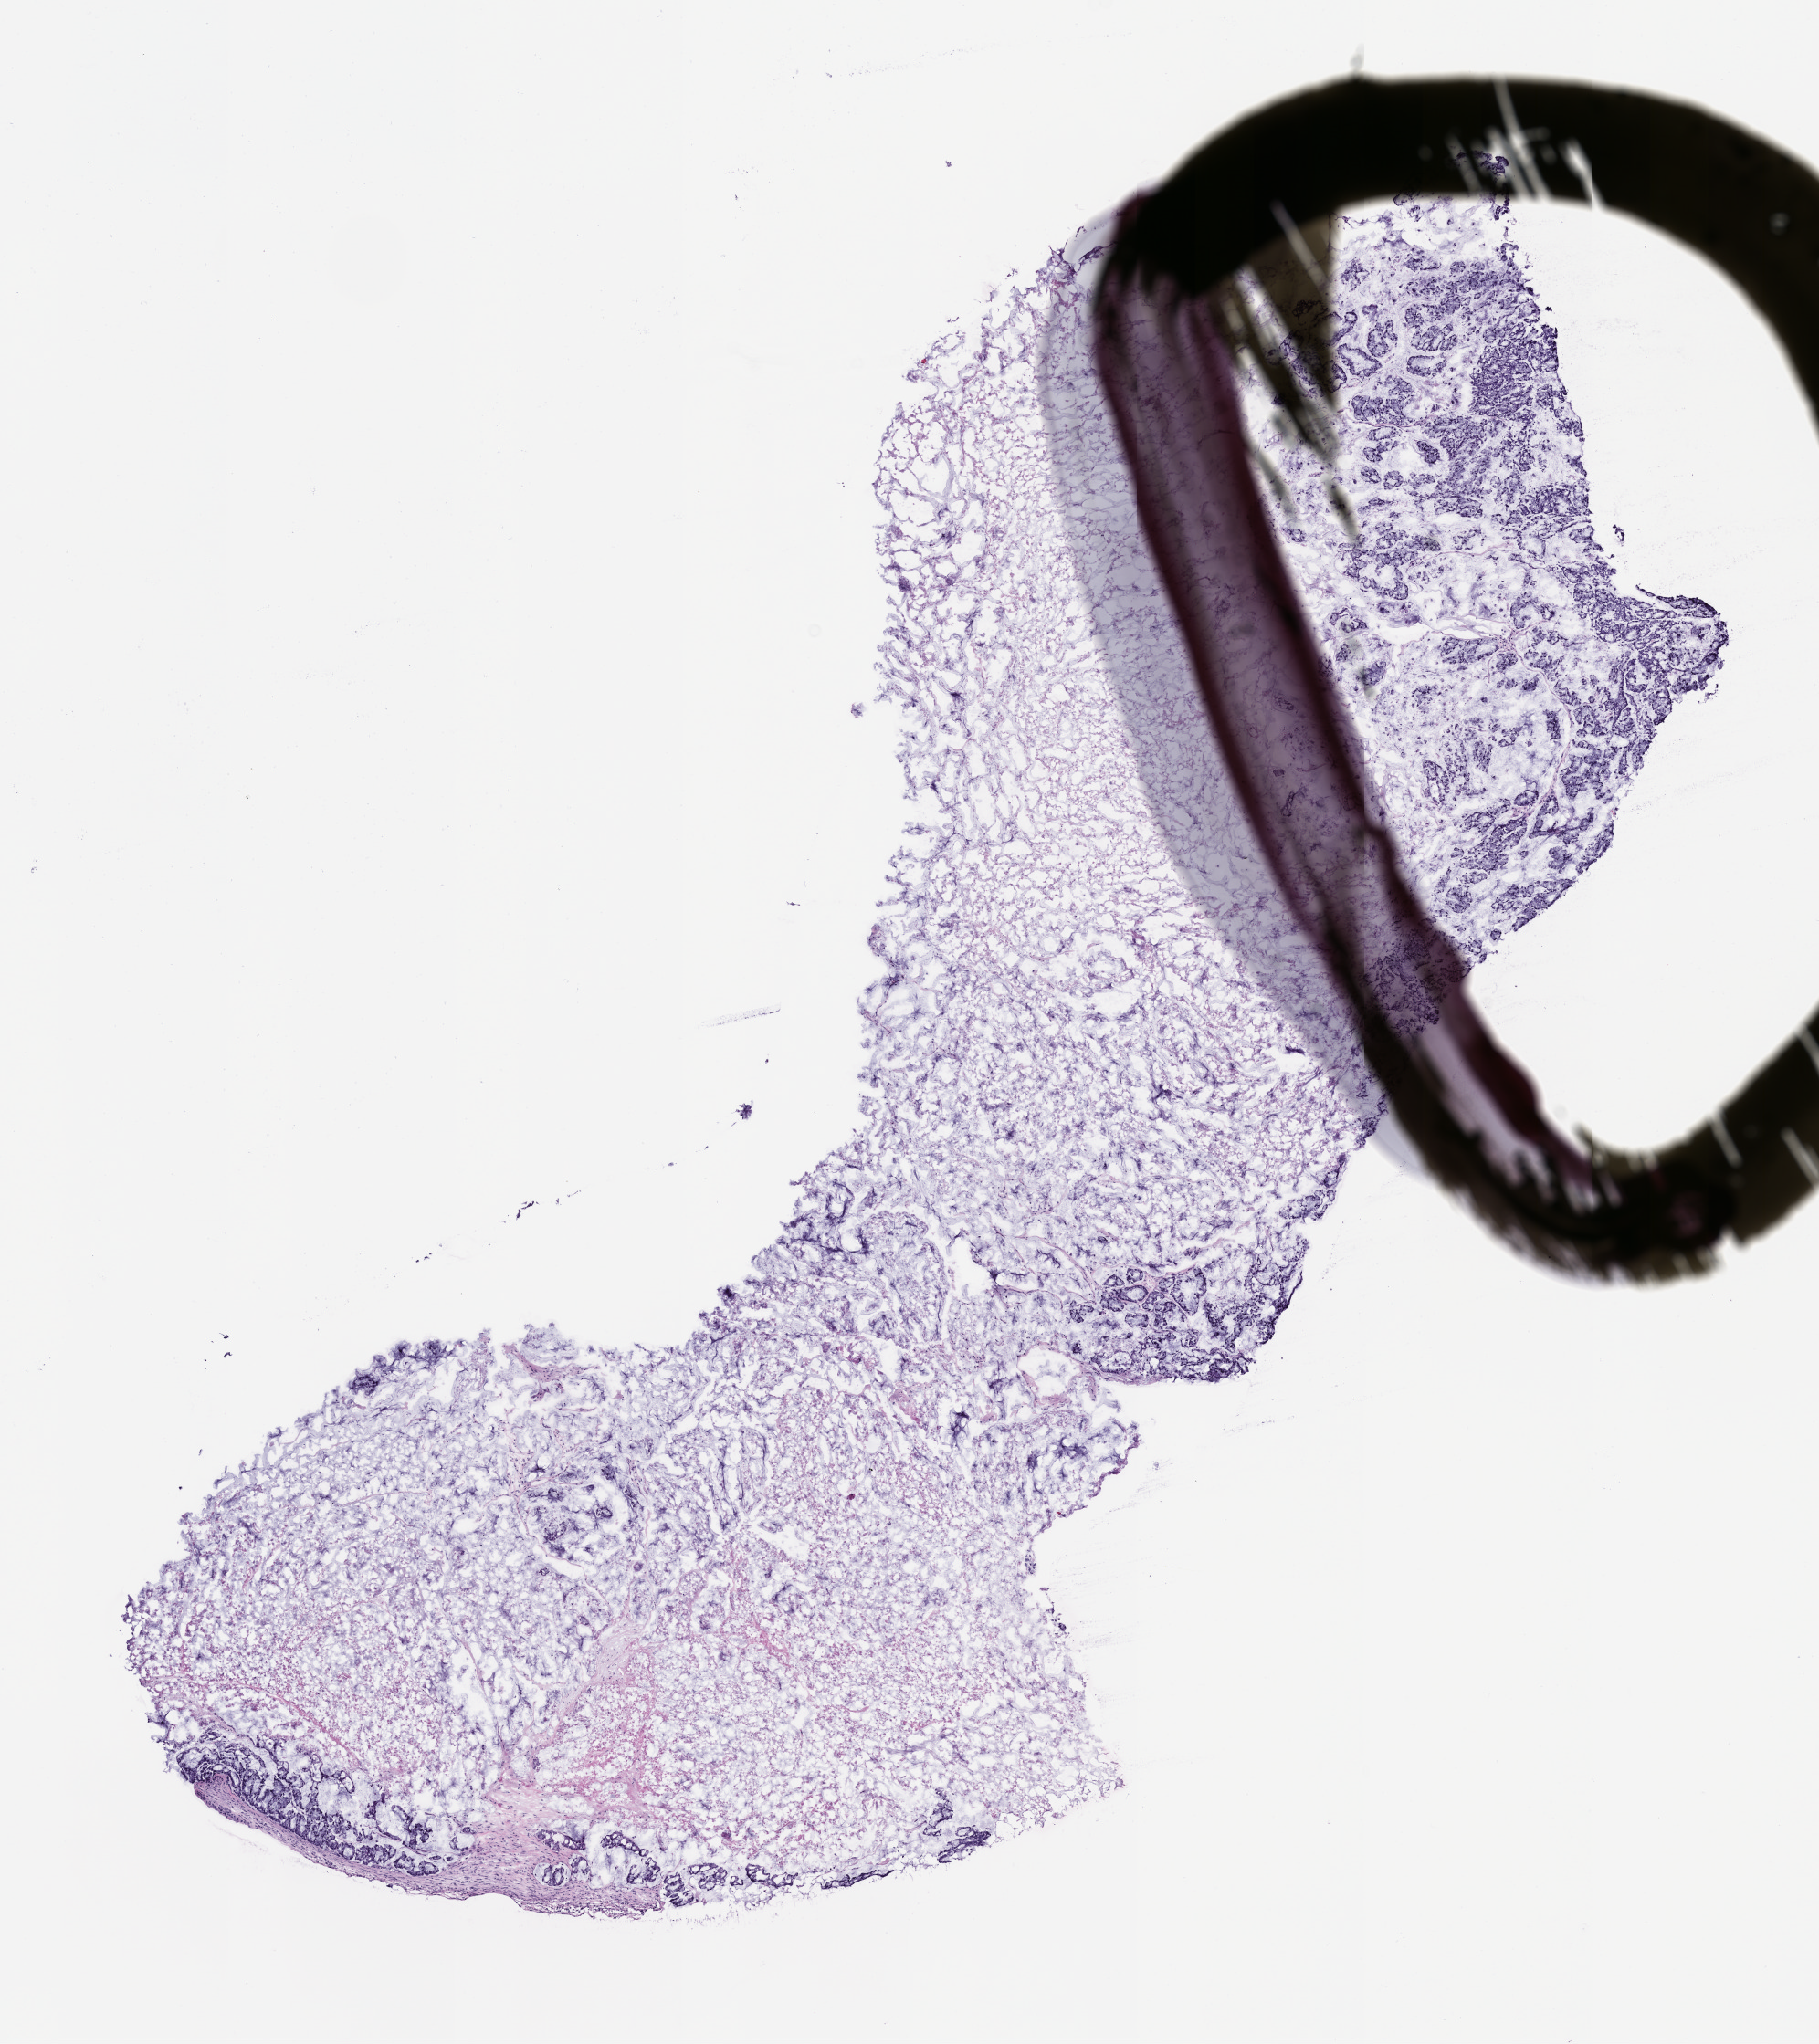
Hematoxylin and eosin (H&E) whole-slide image of a patient-derived xenograft (PDX) tumor grown in a mouse, passage 2 — whole scanned area (about 8.0 x 9.0 mm) shown as a low-resolution overview, formalin-fixed paraffin-embedded section, originating tumor site category: colon.
• originating patient diagnosis: Colon Adenocarcinoma